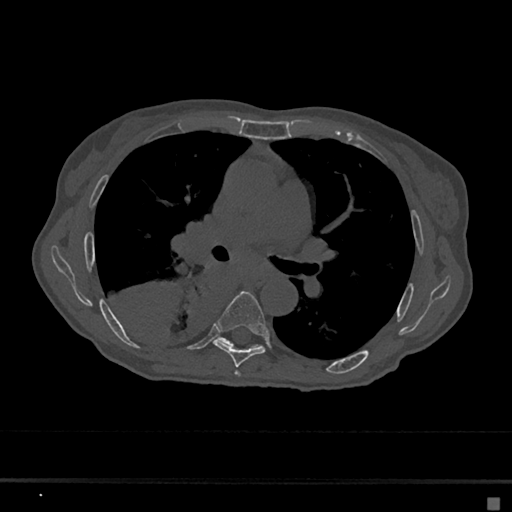
CT including the spine, one axial slice; position 408 of 797 along the scan axis; reconstruction kernel Br40s/3; 120 kVp; bone window (W 1800 / L 400 HU); 0.5 mm slice thickness; 512 × 512 image matrix. Female patient, age 68 years. From the clinical record (not read from this slice): primary cancer: renal.
Annotated regions visible in this slice (semi-automatically segmented with operator editing):
- T5 vertebra: bounding box <235,371,241,377> (left, top, right, bottom; pixels)
- T6 vertebra: <214,291,268,367>
- T7 vertebra: <220,337,259,348>